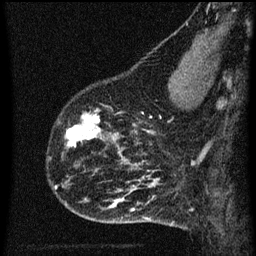
Breast MRI (dynamic contrast-enhanced), one sagittal slice; slice 17 of 60 in the series (ordered by position); dynamic contrast-enhanced series, image 2 of 3 at this slice position (ordered by acquisition); 1.5 T; TE 4.2 ms, TR 8 ms; 2 mm slice thickness; 256 × 256 image matrix. Patient: female, 43 years.
Annotated regions visible in this slice (semi-automatically segmented with operator editing):
- analysis volume of interest (the breast-tissue region the enhancement analysis was run in; not a lesion): bounding box [x1, y1, x2, y2] px = [55, 106, 104, 153]
- tumour enhancement mask (voxels above the 70 % enhancement threshold inside the analysis volume of interest): [66, 108, 102, 147]